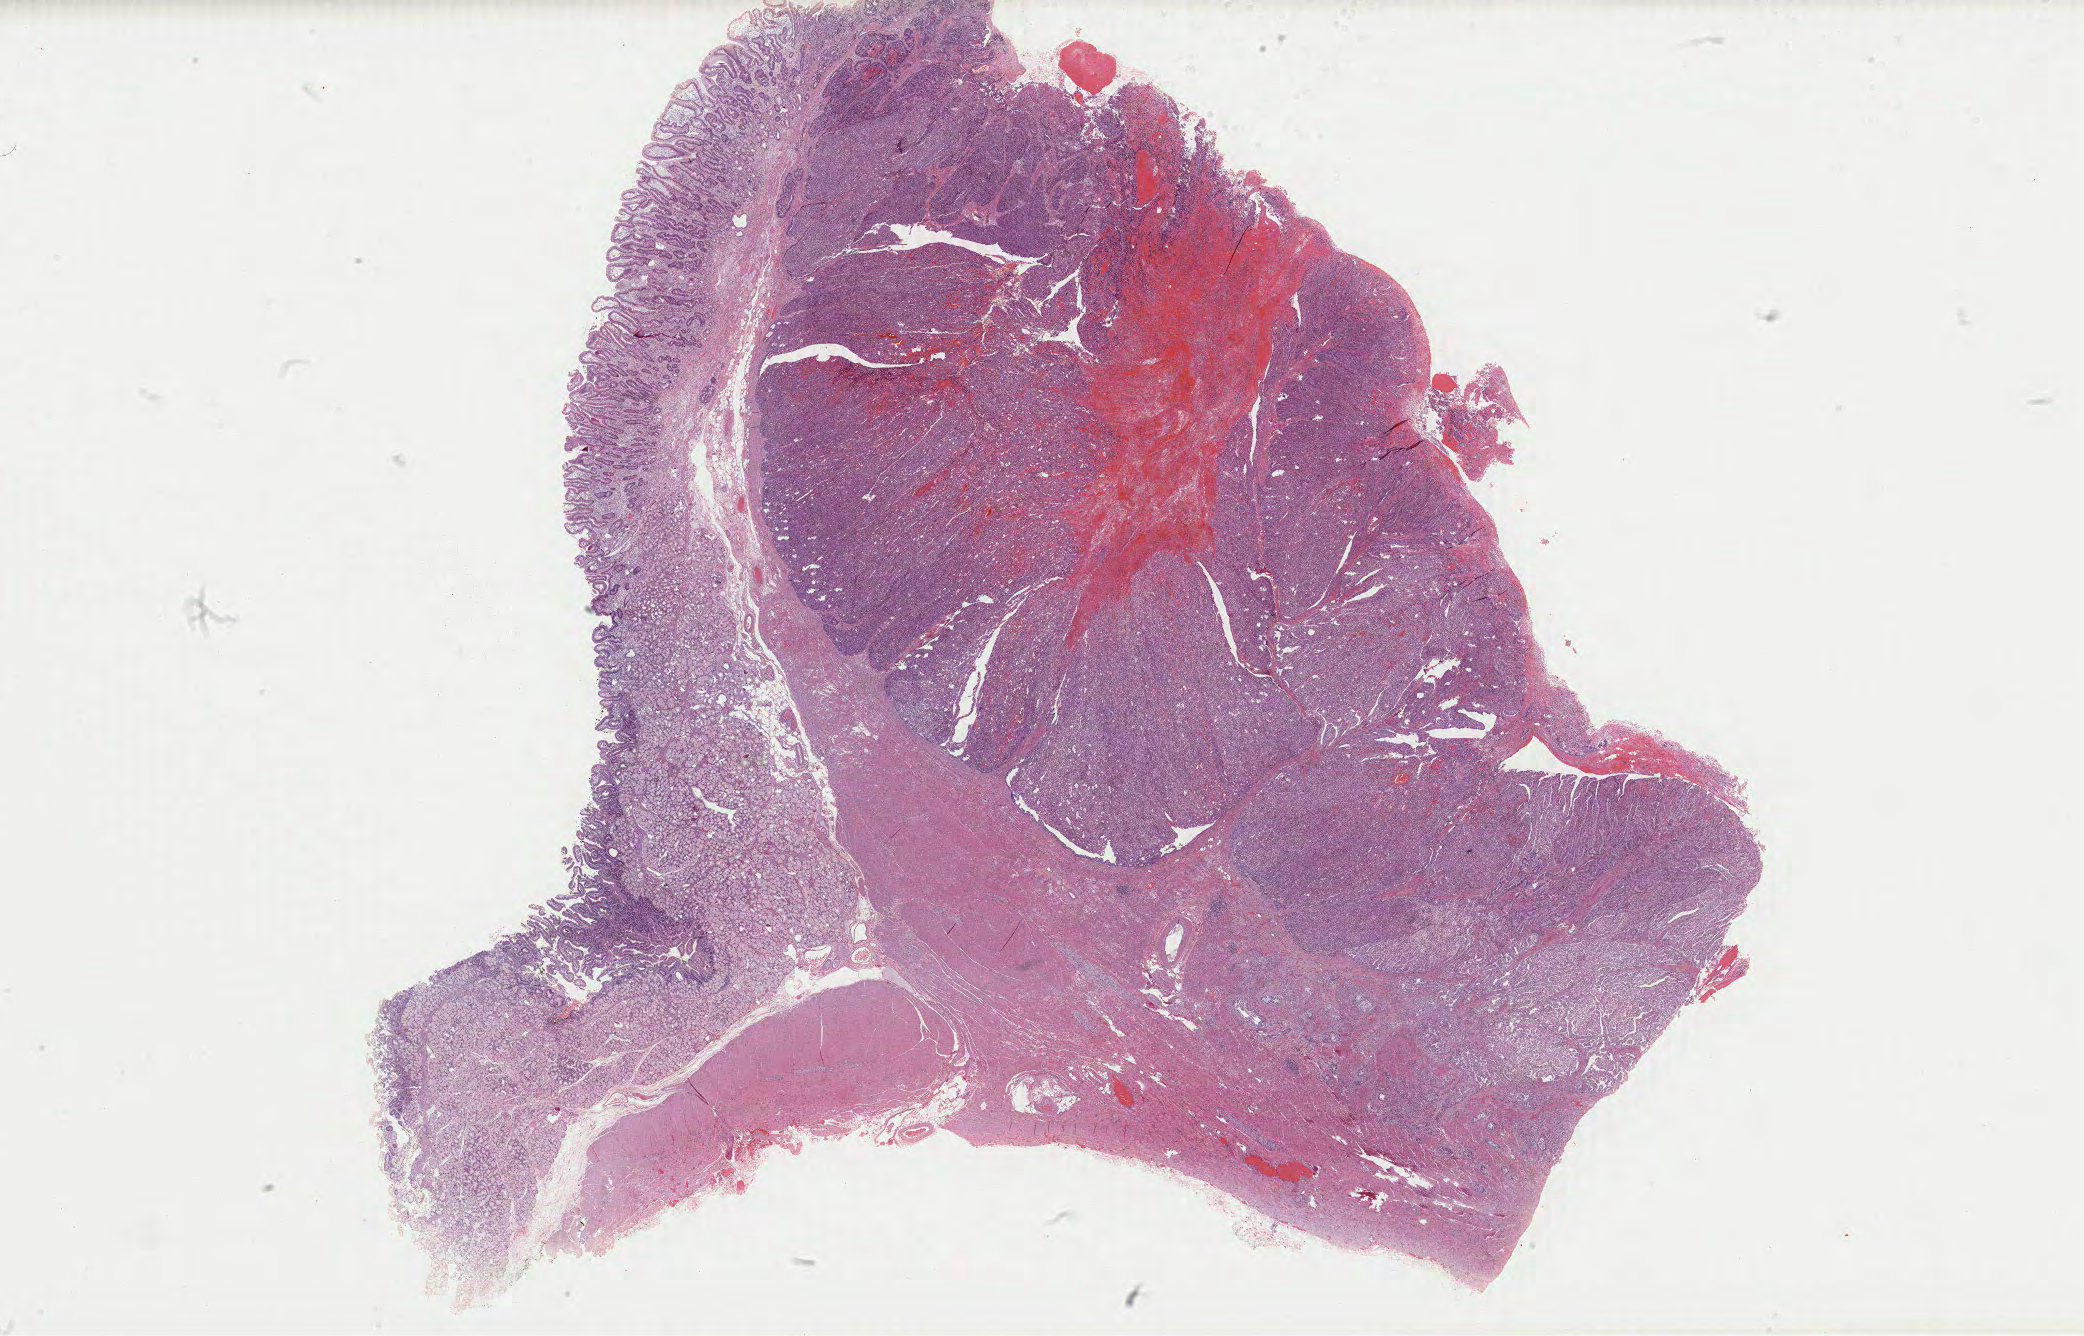
H&E whole-slide image, whole scanned area (about 33.5 x 21.5 mm, slide scanned at 40x) shown as a low-resolution overview; formalin-fixed paraffin-embedded (FFPE) diagnostic section; primary tumour sample from the stomach. Female patient; age at initial diagnosis 78 years.
Histologic diagnosis: Adenocarcinoma, intestinal type.